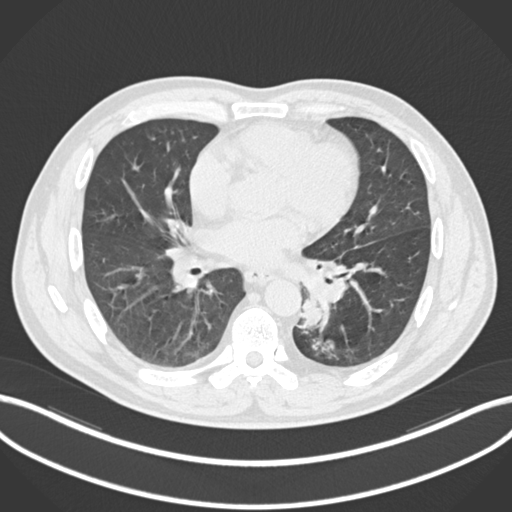
Chest CT, one axial slice. Slice 104 of 223 in the series (ordered by position). Reconstruction kernel B30f. Lung window (W 1500 / L -600 HU). 512 × 512 image matrix, field of view 400 × 400 mm. Male patient, age 50 years. Case-level facts recorded for this patient, not image findings: clinical TNM (as recorded): T2a N3 M0.
Outlined on this slice (bounding box drawn by a radiologist):
- lung tumour (recorded histology: squamous cell carcinoma): bounding box [x1, y1, x2, y2] px = [300, 291, 326, 329]